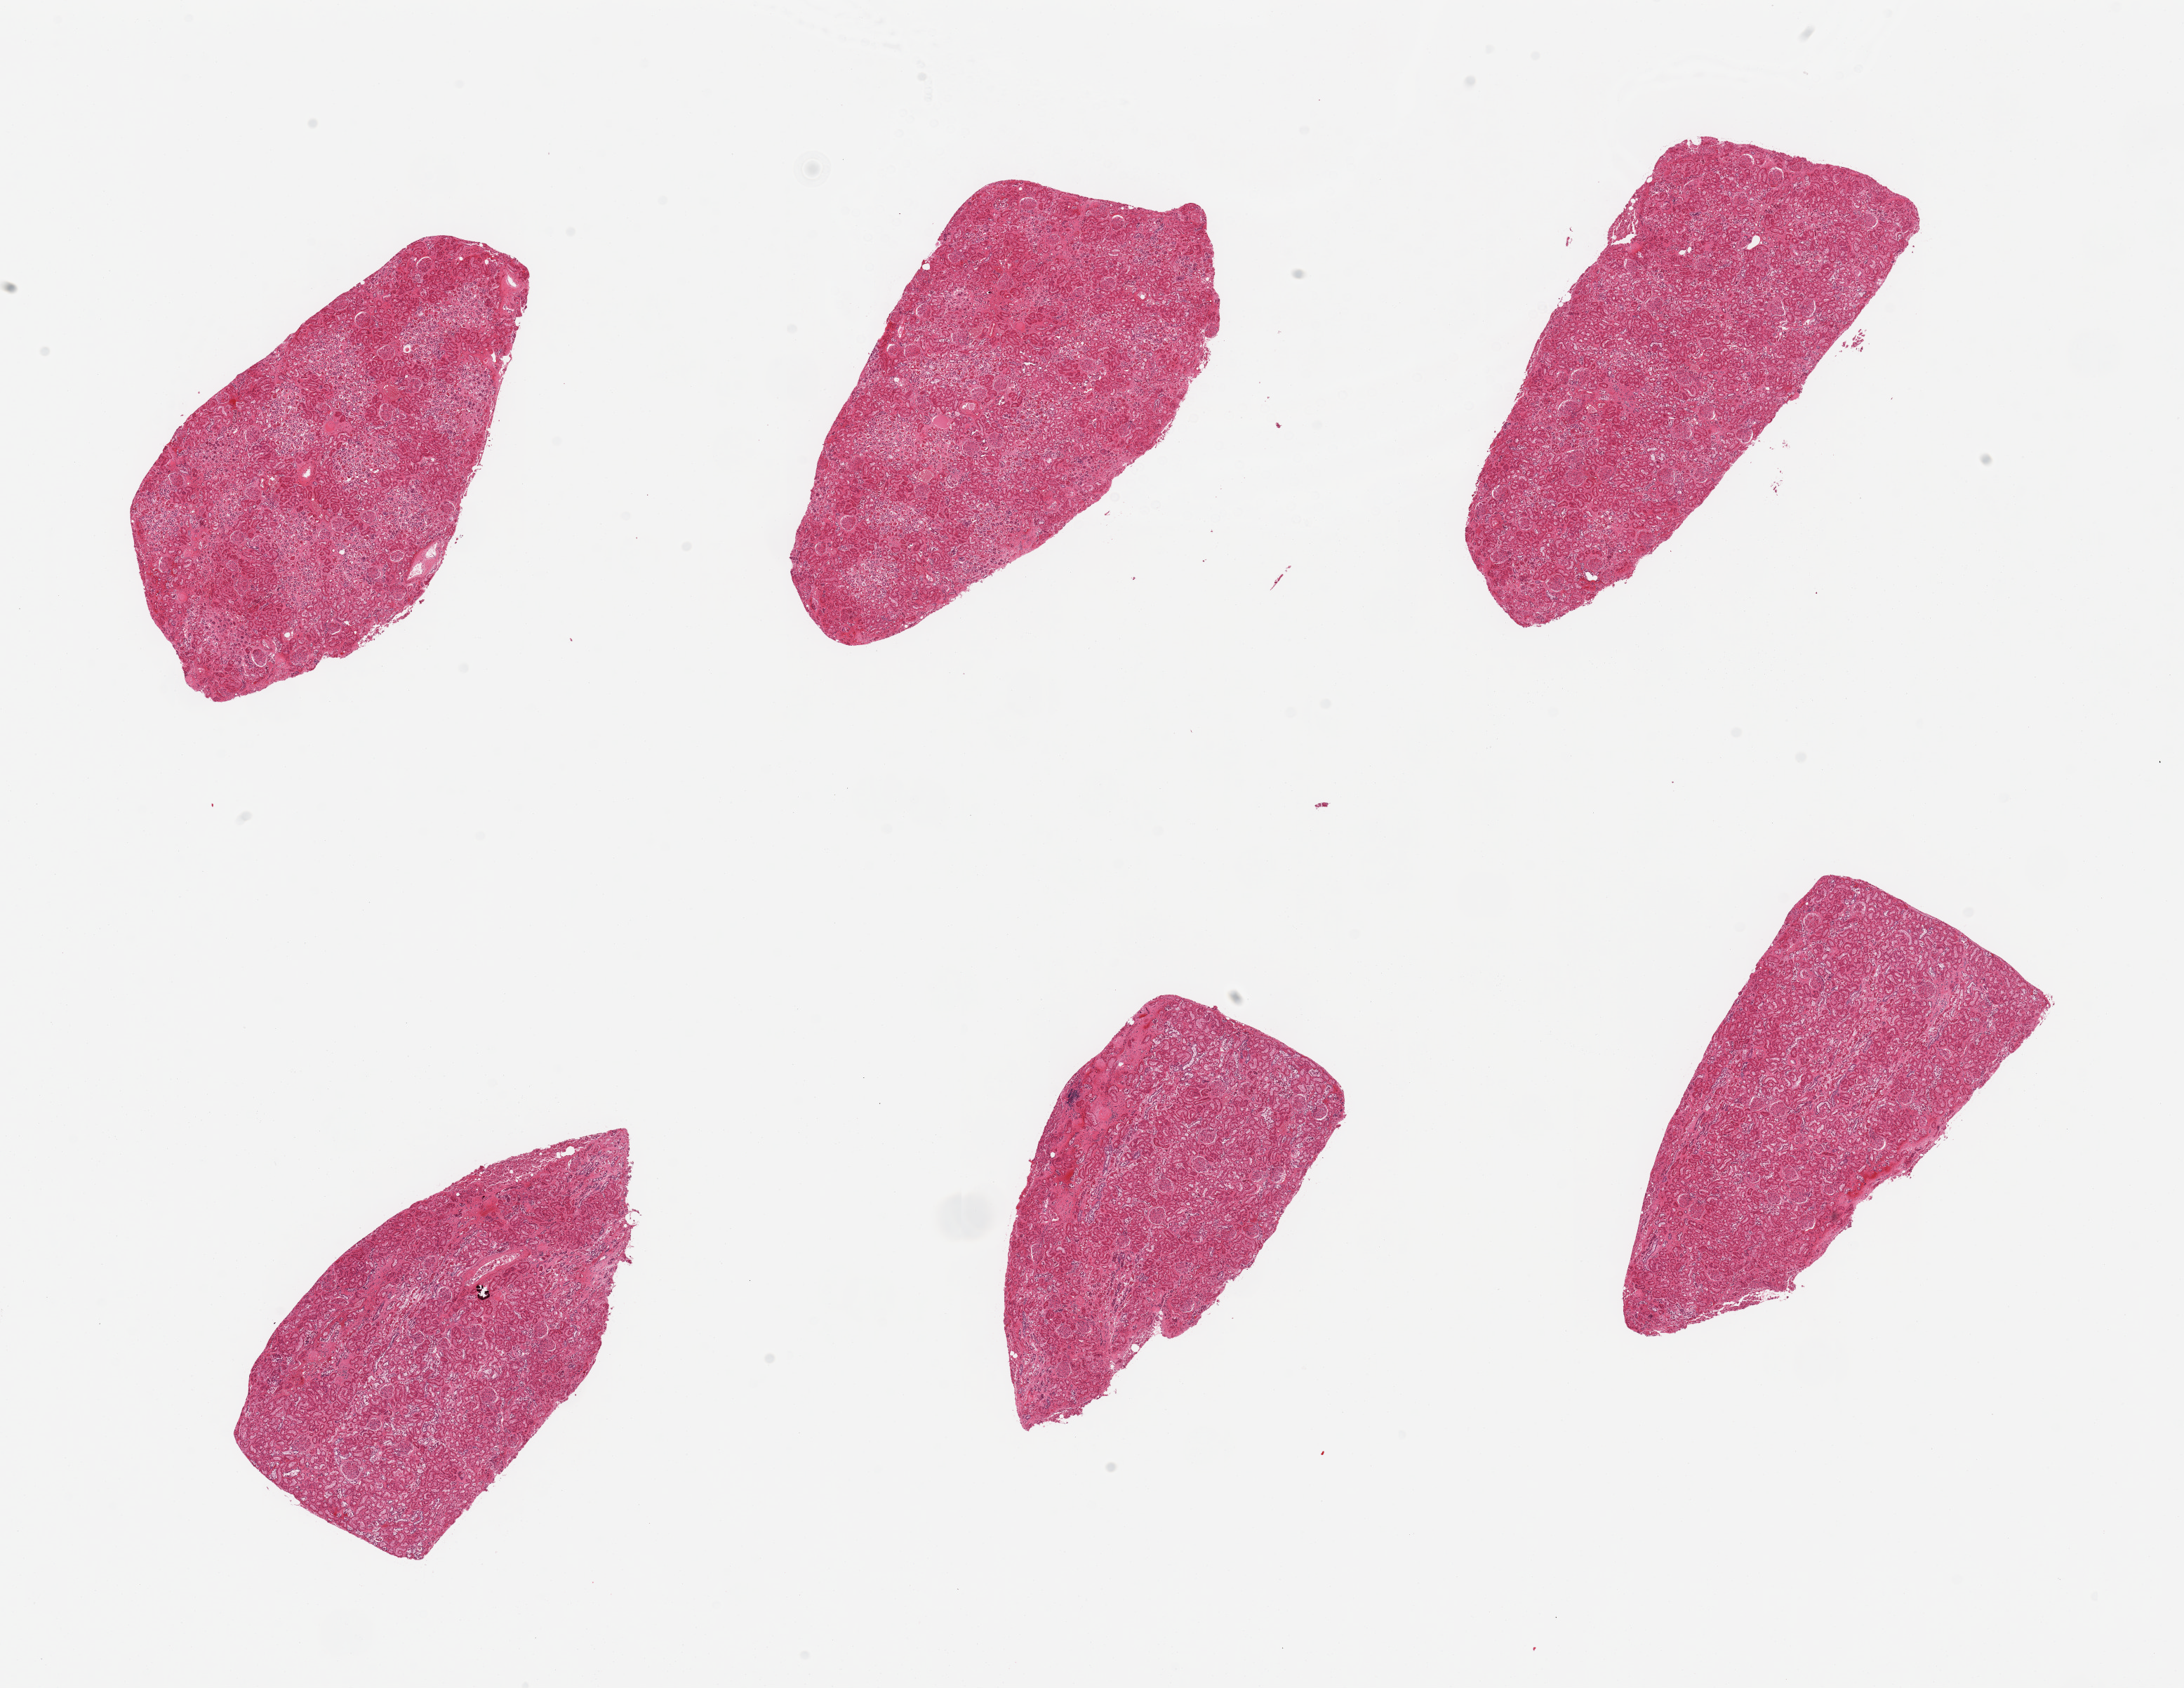
Digitized hematoxylin and eosin (H&E)-stained section — low-resolution overview of the scanned area, about 24.6 x 19.0 mm (slide scanned at 20x). PAXgene-fixed paraffin-embedded (PFPE) section. Sampled site (target tissue): renal cortex. Donor tissue sample. Donor: male.
* review note (as recorded): 6 pieces; no active or chronic lesions